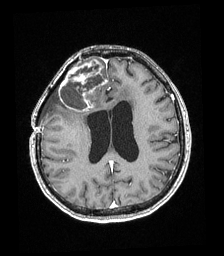
Brain MRI from a brain-tumour surgery series, one axial slice. Position 80 of 192 along the scan axis. T1-weighted post-contrast. 1 mm slice thickness. 224 × 256 image matrix. Case-level facts recorded for this patient, not image findings: histopathology: Astrocytoma; WHO grade: 4.
Annotated regions visible in this slice (outlined manually by an expert reader):
- tumour: box from (x=59, y=60) to (x=106, y=112) px